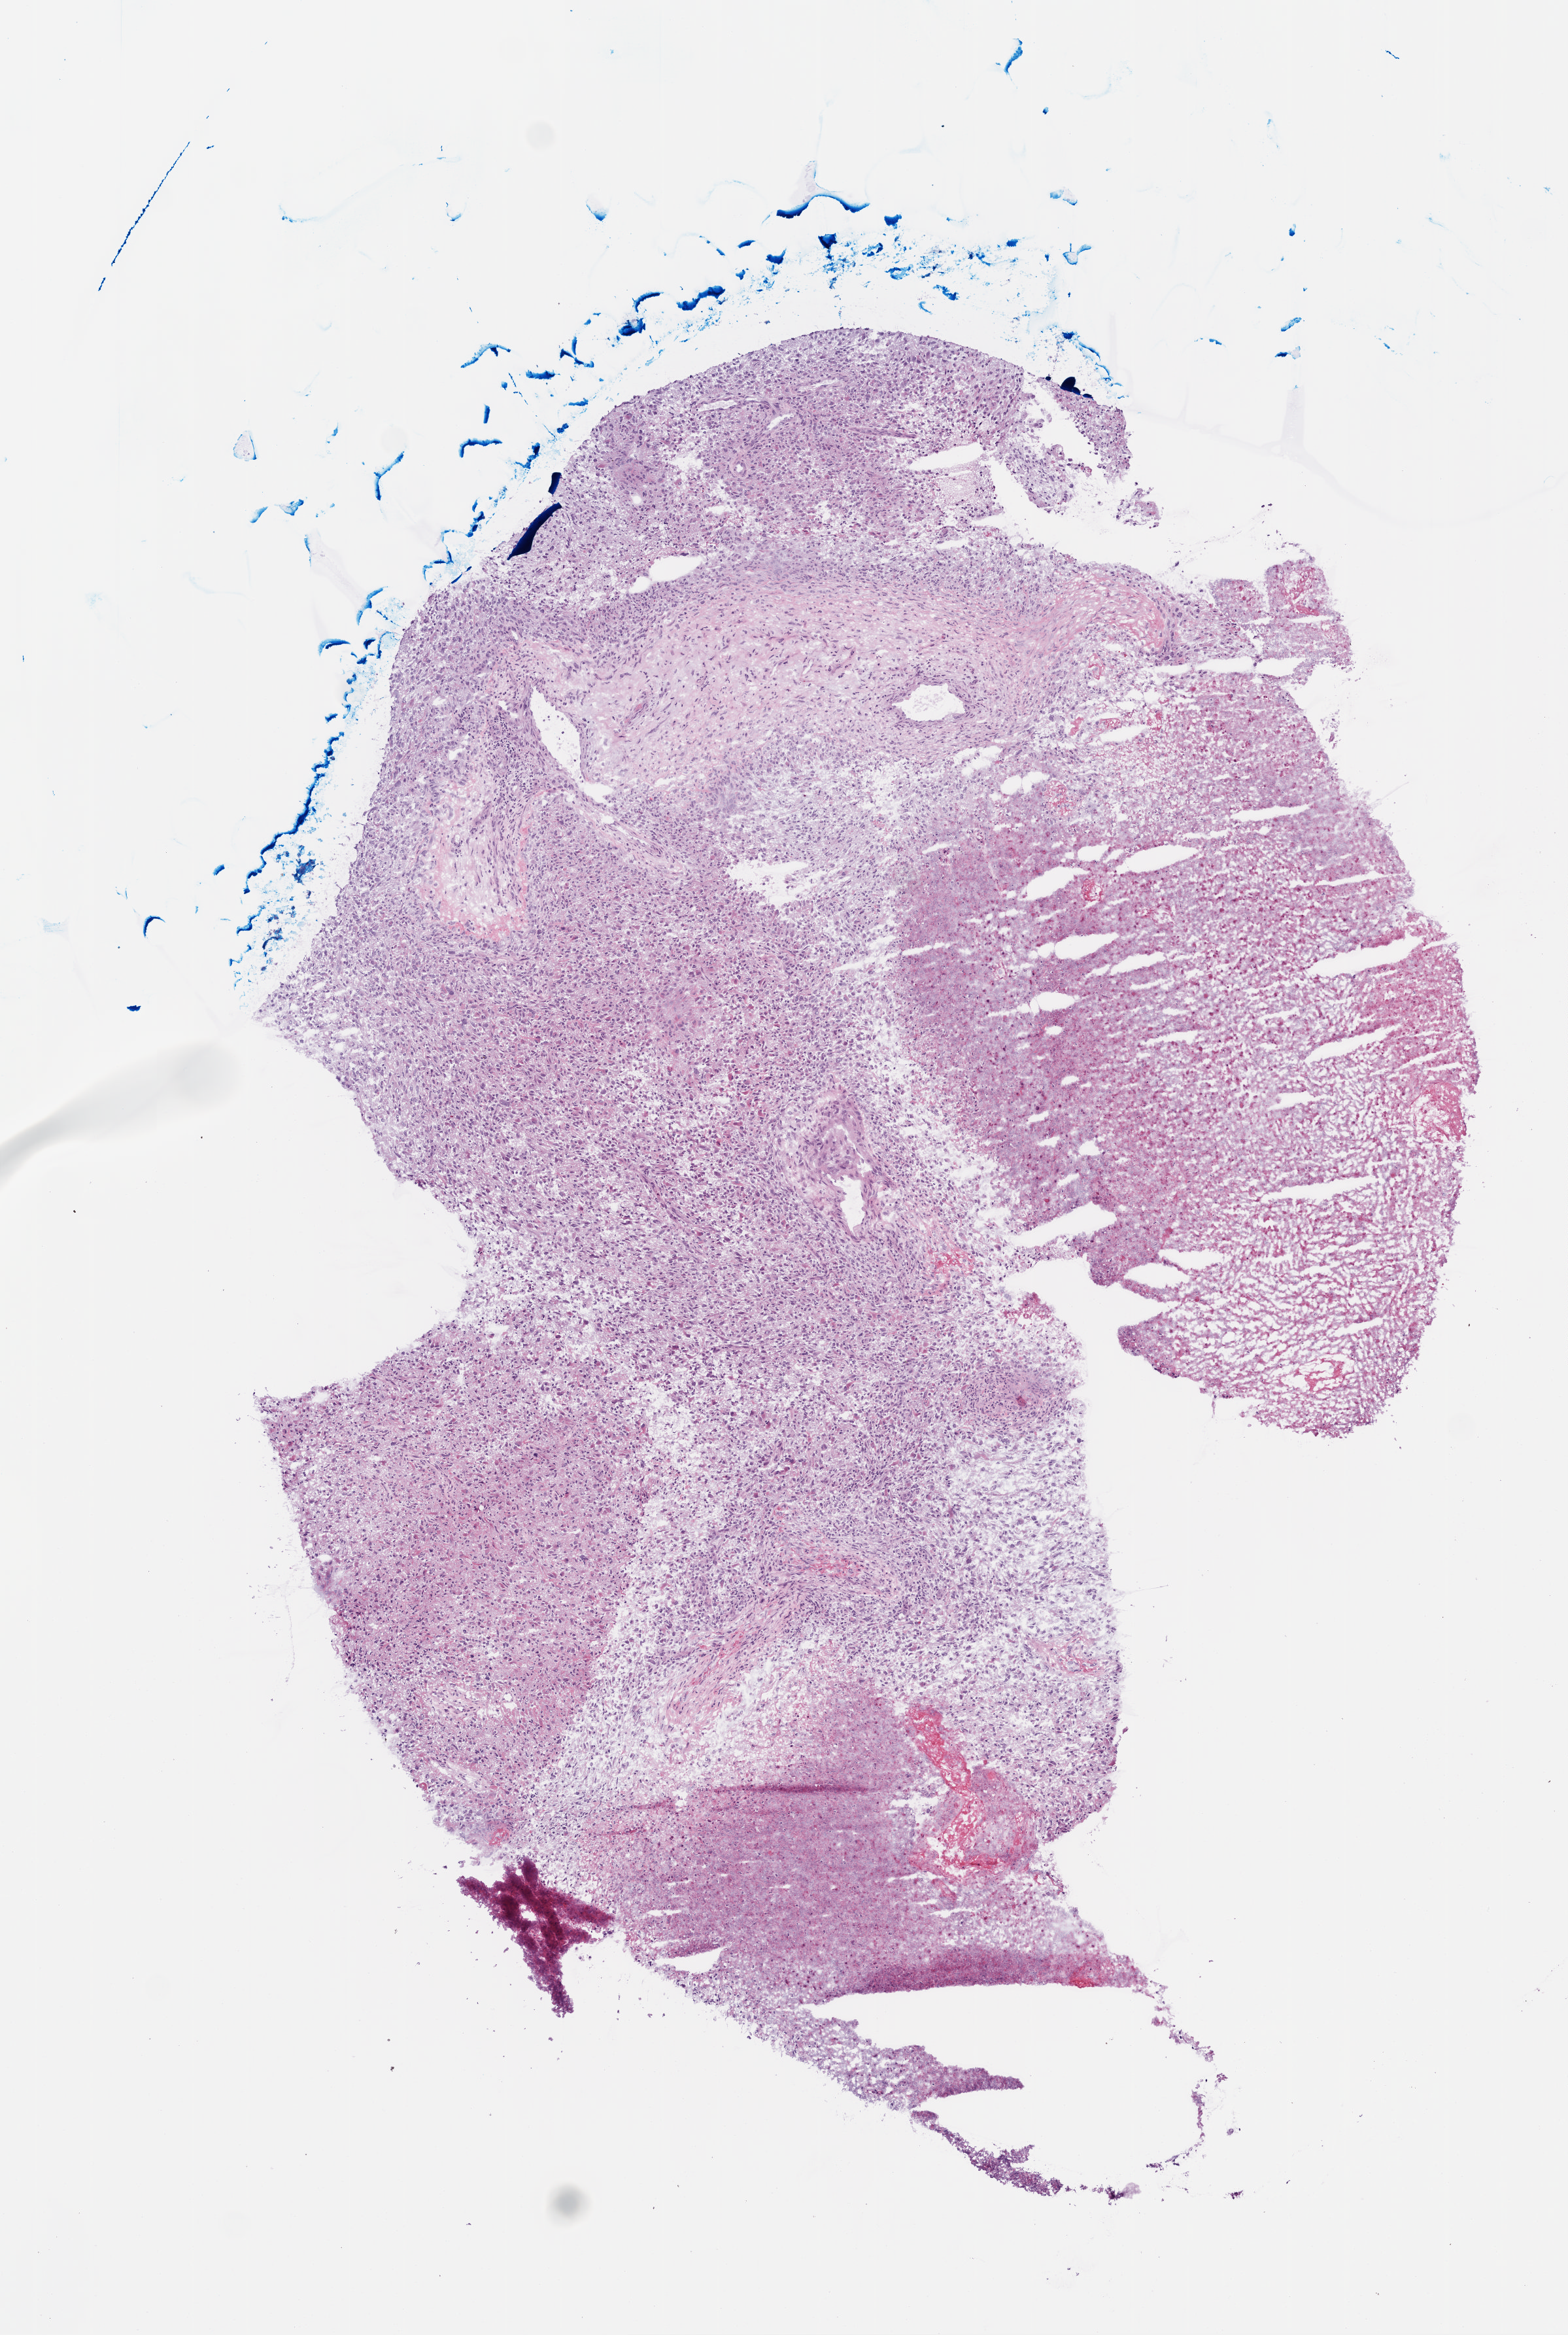
Digitized Hematoxylin and eosin (H&E) stained tissue section (whole slide) — a low-resolution overview of the entire scanned area, about 4.8 x 7.2 mm; frozen section from the top of the tissue portion; sample: primary tumour, brain. Female patient; age at initial diagnosis 73 years.
Histologic diagnosis: Glioblastoma.